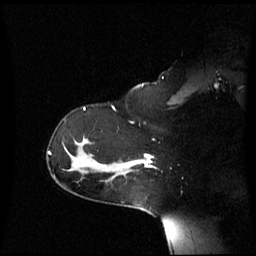
Breast MRI (dynamic contrast-enhanced), one sagittal slice. Slice 45 of 60 in the series (ordered by position). Dynamic contrast-enhanced series, image 2 of 3 at this slice position (ordered by acquisition). 1.5 T. TE 4.2 ms, TR 8.4 ms. 256 × 256 image matrix, field of view 270 × 270 mm. Female patient, age 39 years. Case-level facts recorded for this patient, not image findings: setting: breast cancer imaged before/during neoadjuvant chemotherapy; receptor status: triple-negative.
Structures marked on this image (semi-automatically segmented with operator editing):
- analysis volume of interest (the breast-tissue region the enhancement analysis was run in; not a lesion): bounding box (x1, y1, x2, y2) in pixels: (117, 154, 152, 176)
- tumour enhancement mask (voxels above the 70 % enhancement threshold inside the analysis volume of interest): (132, 154, 152, 167)